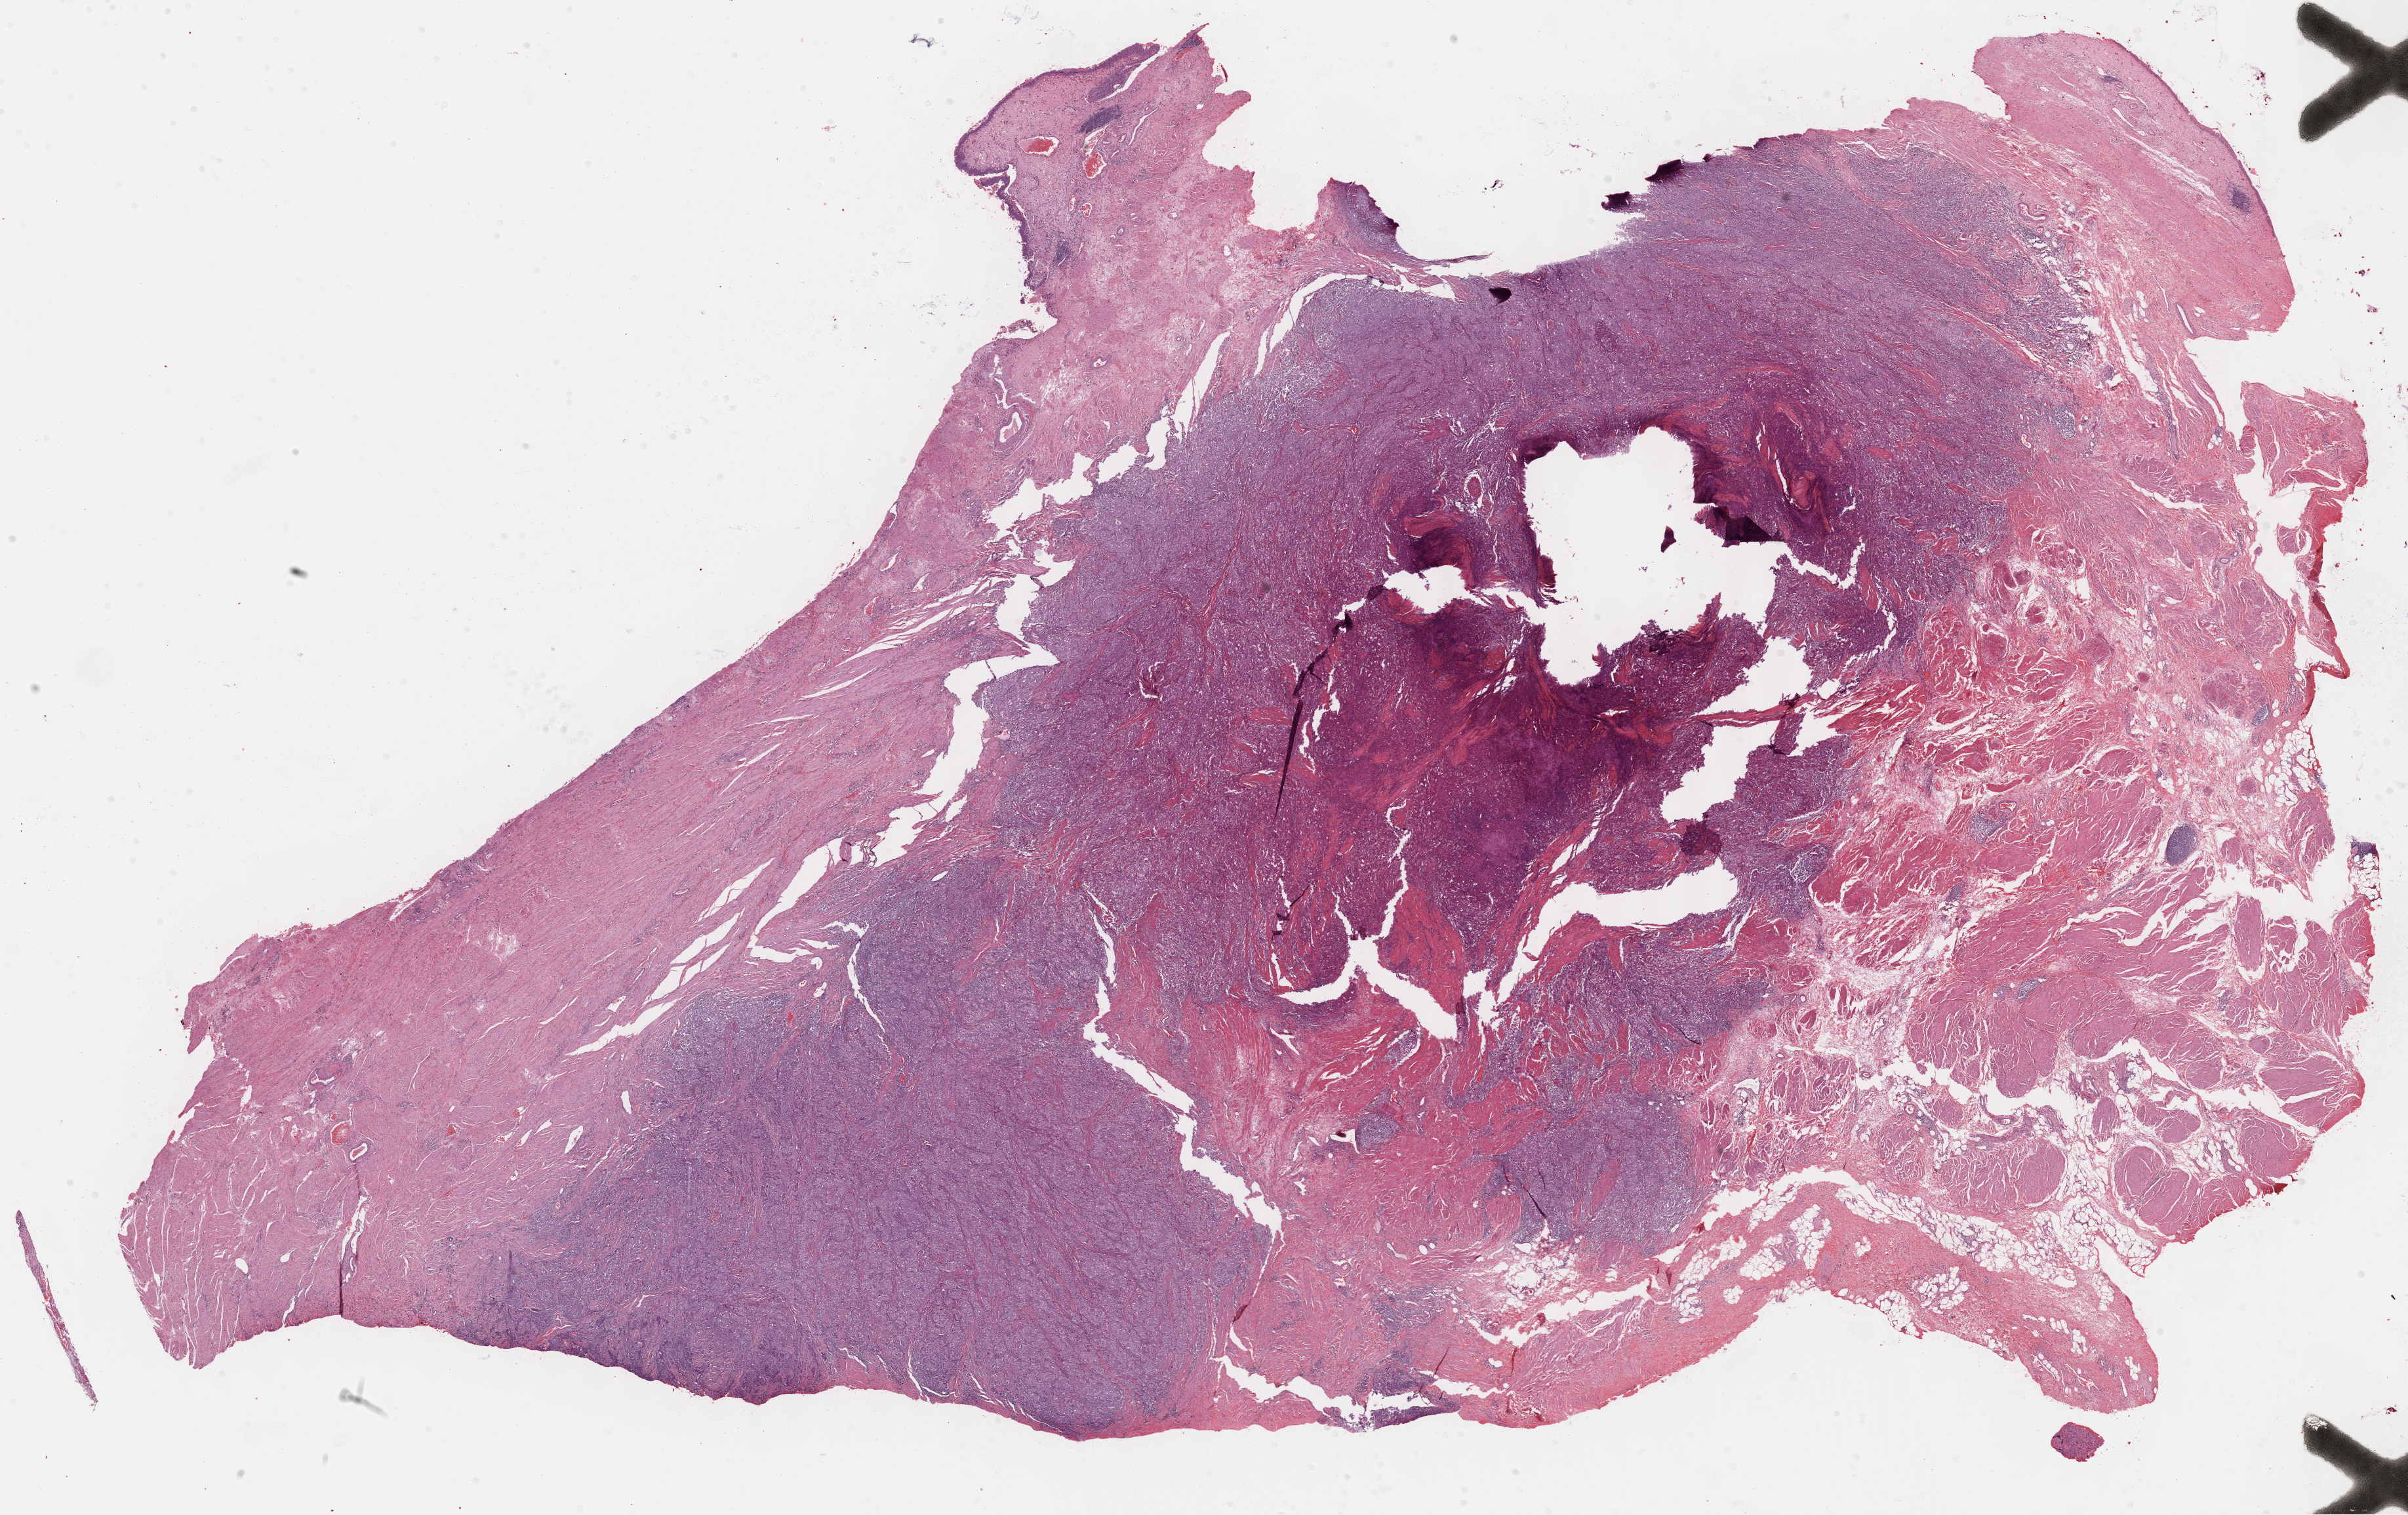
Digitized H&E-stained tissue section (whole slide) — shown as a low-resolution overview of the whole scanned area (about 29.7 x 18.7 mm), formalin-fixed paraffin-embedded (FFPE) diagnostic section, sample: primary tumour, bladder. Female patient; age at initial diagnosis 73 years.
Diagnosis: Papillary transitional cell carcinoma.